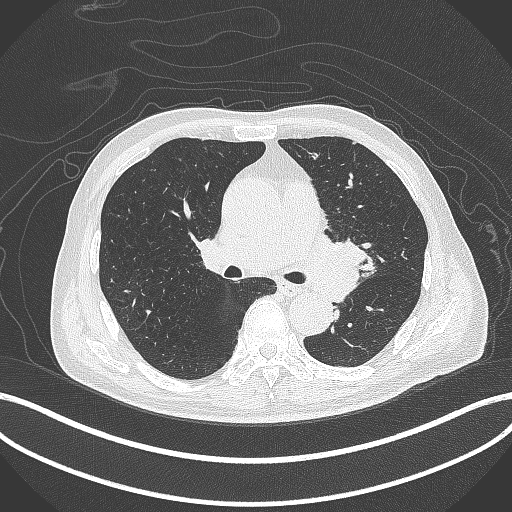
Chest CT, one axial slice; reconstruction kernel B70f; 120 kVp; lung window (W 1500 / L -600 HU); 1 mm slice thickness; 512 × 512 image matrix, field of view 400 × 400 mm. Patient: male, 77 years. Case-level facts recorded for this patient, not image findings: clinical TNM (as recorded): T3 N1 M0.
Outlined on this slice (rectangle marked by the reading radiologist):
- lung tumour (recorded histology: adenocarcinoma): bounding box <306,226,374,299> (left, top, right, bottom; pixels)